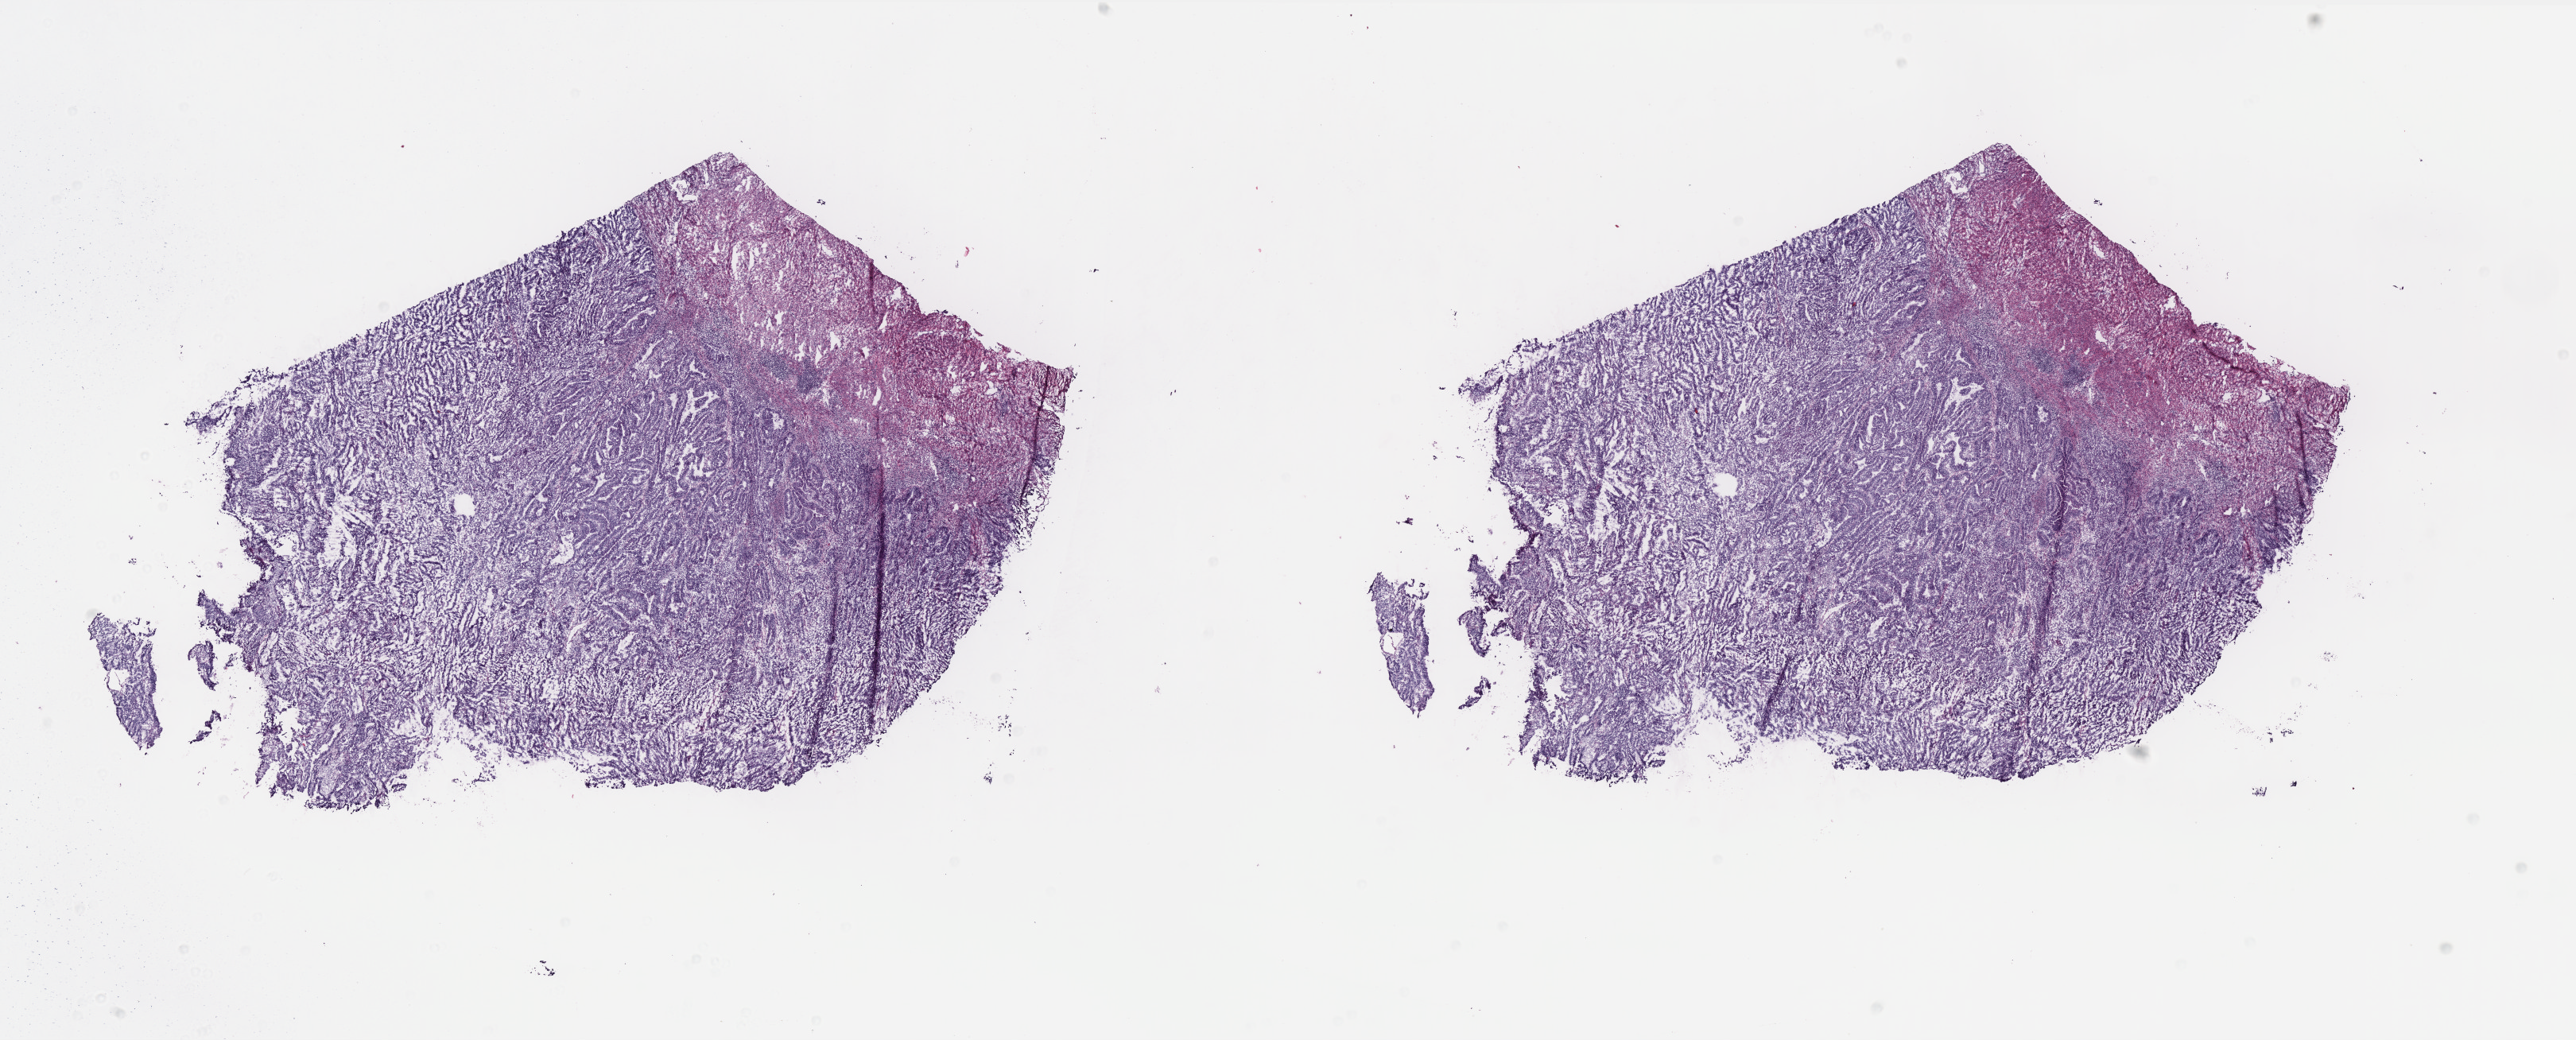
Hematoxylin and eosin (H&E) stained whole-slide image — a low-resolution overview of the entire scanned area, about 26.0 x 10.5 mm; frozen section from the top of the tissue portion; primary tumour sample from the uterus. Patient: female, age at initial diagnosis 76 years. Histologic grade: G1 (well differentiated). Composition of this section per pathologist review: tumour cells 80%, tumour nuclei 70%, normal cells 20%, stromal cells 0%, necrosis 0%. Inflammatory infiltration, as recorded: lymphocyte infiltration 0%, monocyte infiltration 0%, neutrophil infiltration 0%.
• FIGO stage: IA
• diagnosis: Endometrioid adenocarcinoma, NOS (endometrium)